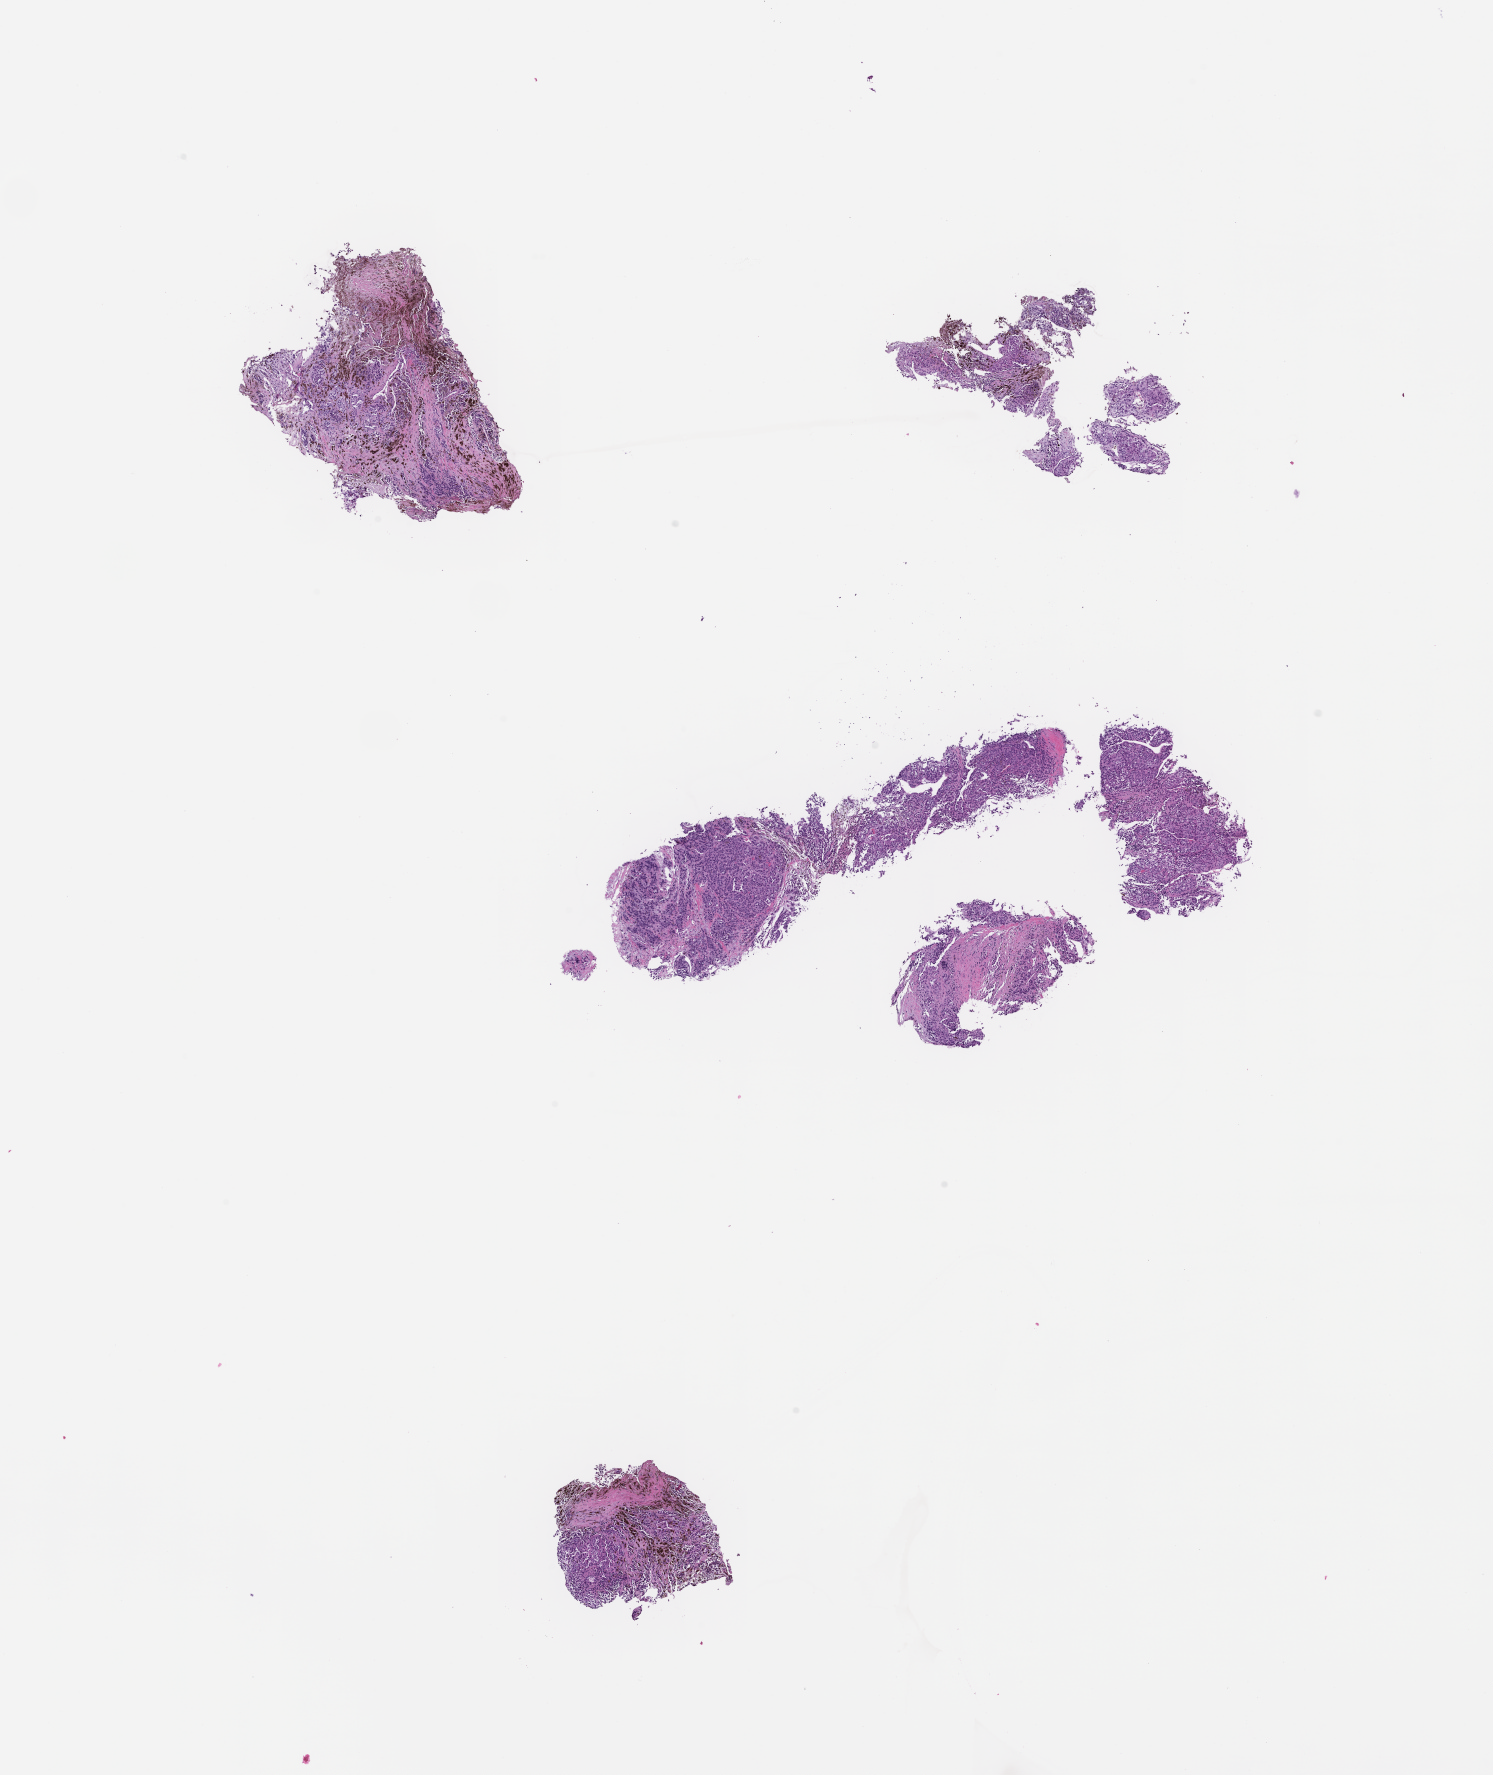
Haematoxylin and eosin whole-slide image — a low-resolution overview of the entire scanned area, about 12.1 x 14.3 mm, FFPE section, collected at baseline (before treatment). Patient sex: female.
This section: metastasis (sampled organ not recorded). Primary diagnosis of the patient: Melanoma.